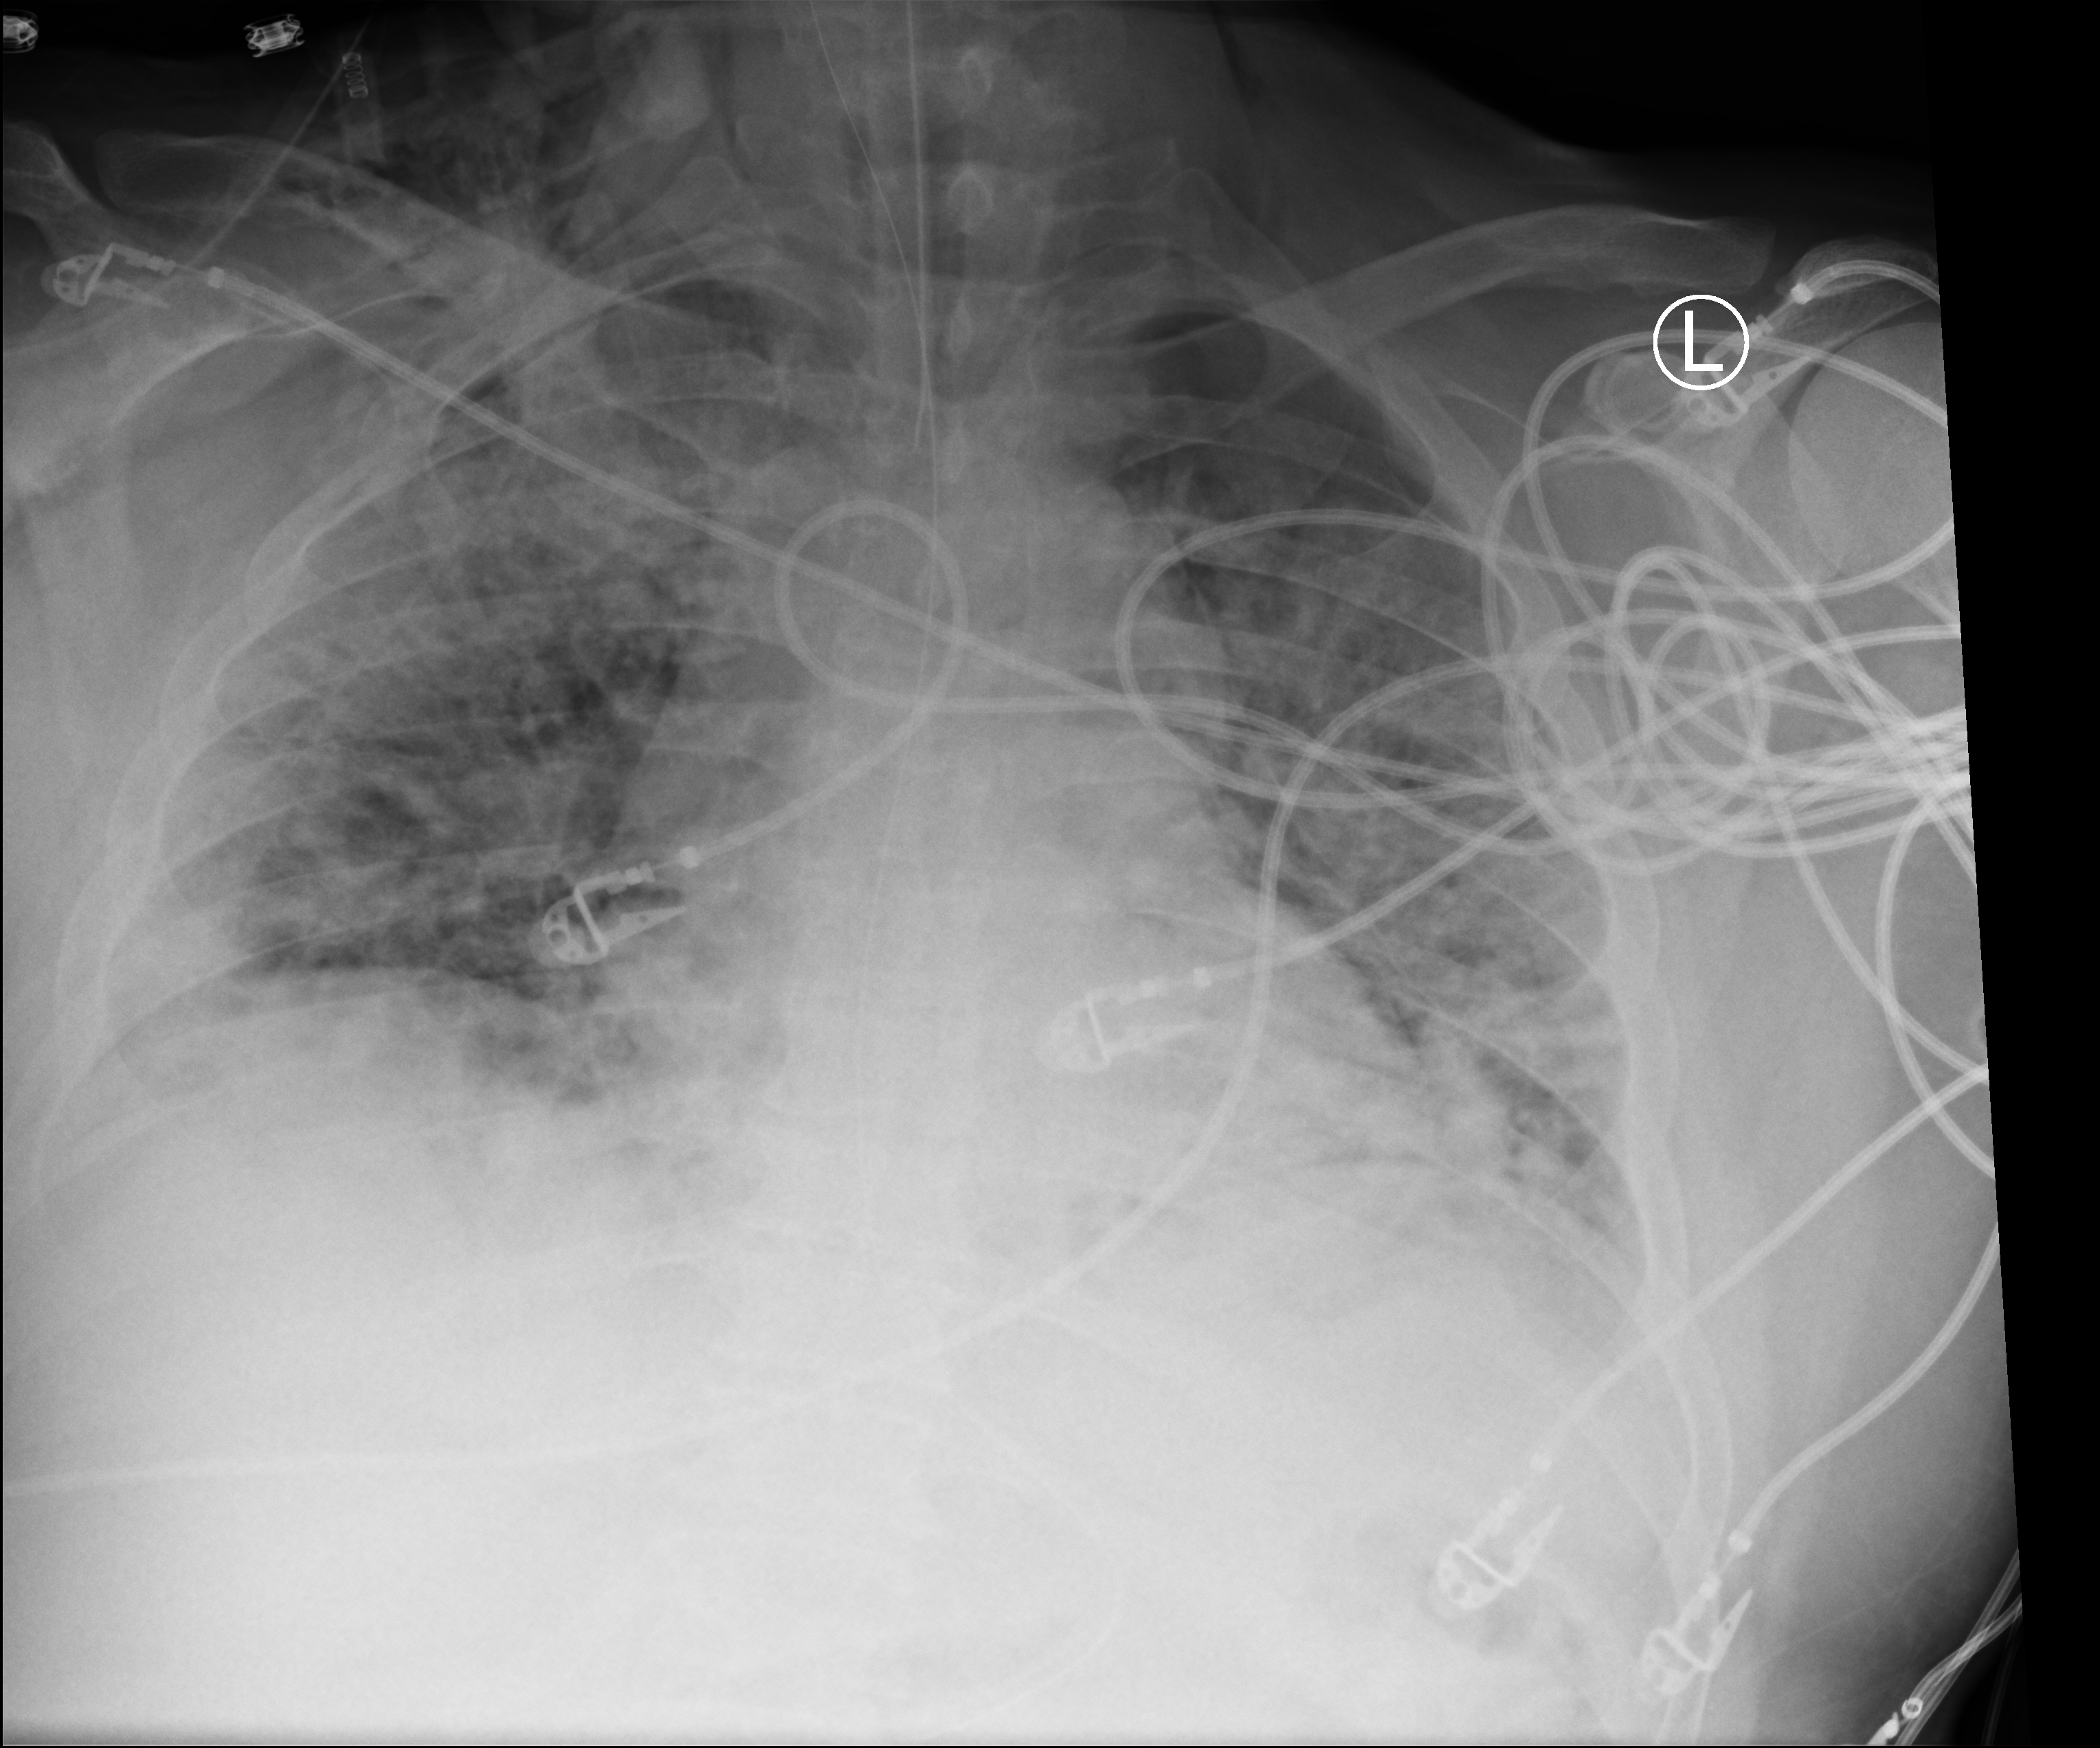
Bedside chest radiograph (computed radiography); anteroposterior (AP) projection. Patient hospitalised with COVID-19, aged 18–59 years.
From the hospital-stay record, not from the radiograph (when in the stay this image was taken is not recorded): mechanically ventilated during this hospital stay: yes.